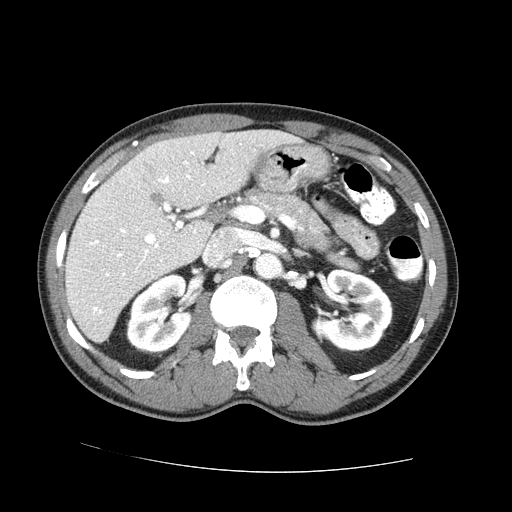
Contrast-enhanced abdominal CT (liver protocol), one axial slice. One of 2 acquisitions stored at this slice position. Soft-tissue window (W 400 / L 40 HU). 2.5 mm slice thickness. 512 × 512 image matrix, field of view 380 × 380 mm. From the clinical record (not read from this slice): diagnosis: hepatocellular carcinoma (patient treated with transarterial chemoembolisation; whether this scan precedes or follows treatment is not stated here); TNM stage (as recorded): Stage-IVA; Child-Pugh class: A; tumour nodularity: uninodular.
Structures marked on this image (semi-automatic segmentation, software-assisted and operator-edited):
- liver parenchyma outside the tumour (the mass and vessels are separate outlines, so this box may not span the whole liver): bounding box <65,130,302,342> (left, top, right, bottom; pixels)
- mass: <151,192,164,207>
- liver vessels: <90,151,196,314>